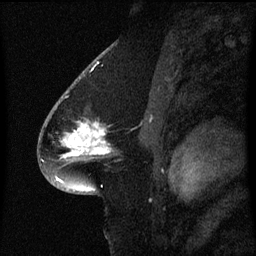
Breast MRI (dynamic contrast-enhanced), one sagittal slice. Slice 37 of 60 in the series (ordered by position). Dynamic contrast-enhanced series, image 2 of 3 at this slice position (ordered by acquisition). 1.5 T. TE 4.2 ms, TR 8.4 ms. 2 mm slice thickness. 256 × 256 image matrix, field of view 200 × 200 mm. Female patient, age 54 years. From the clinical record (not read from this slice): setting: breast cancer imaged before/during neoadjuvant chemotherapy; receptor status: HR-positive, HER2-negative.
Annotated regions visible in this slice (semi-automatic segmentation, software-assisted and operator-edited):
- analysis volume of interest (the breast-tissue region the enhancement analysis was run in; not a lesion): box from (x=46, y=100) to (x=111, y=171) px
- tumour enhancement mask (voxels above the 70 % enhancement threshold inside the analysis volume of interest): (x=64, y=124)–(x=110, y=157)